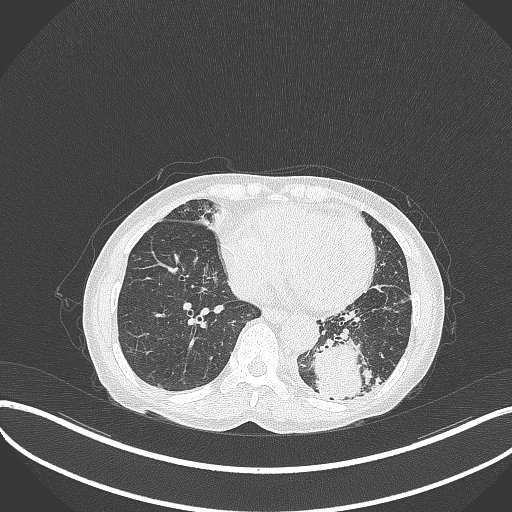
Chest CT, one axial slice. Slice 95 of 370 in the series (ordered by position). Reconstruction kernel B70f. 120 kVp. Lung window (W 1500 / L -600 HU). 1 mm slice thickness. 512 × 512 image matrix, field of view 400 × 400 mm. Patient: female, 78 years. Case-level facts recorded for this patient, not image findings: clinical TNM (as recorded): T3 N0 M1.
Annotated regions visible in this slice (bounding box drawn by a radiologist):
- lung tumour (recorded histology: squamous cell carcinoma): bounding box (x1, y1, x2, y2) in pixels: (310, 334, 371, 403)